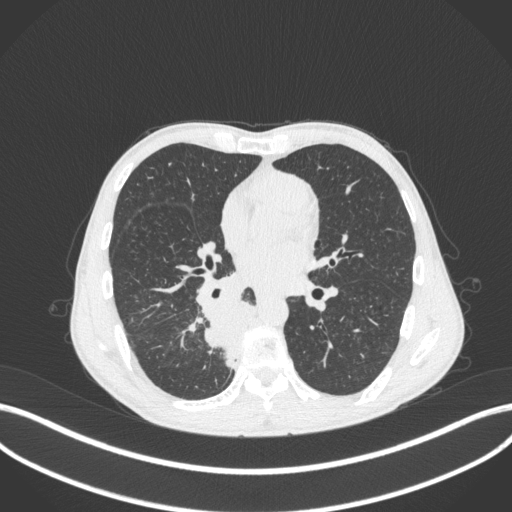
Chest CT, one axial slice; slice 184 of 371 in the series (ordered by position); reconstruction kernel B31f; 120 kVp; lung window (W 1500 / L -600 HU); 512 × 512 image matrix. Male patient, age 58 years. Case-level facts recorded for this patient, not image findings: clinical TNM (as recorded): T3 N1 M1.
Structures marked on this image (bounding box drawn by a radiologist):
- lung tumour (recorded histology: squamous cell carcinoma): bounding box [x1, y1, x2, y2] px = [196, 297, 256, 368]